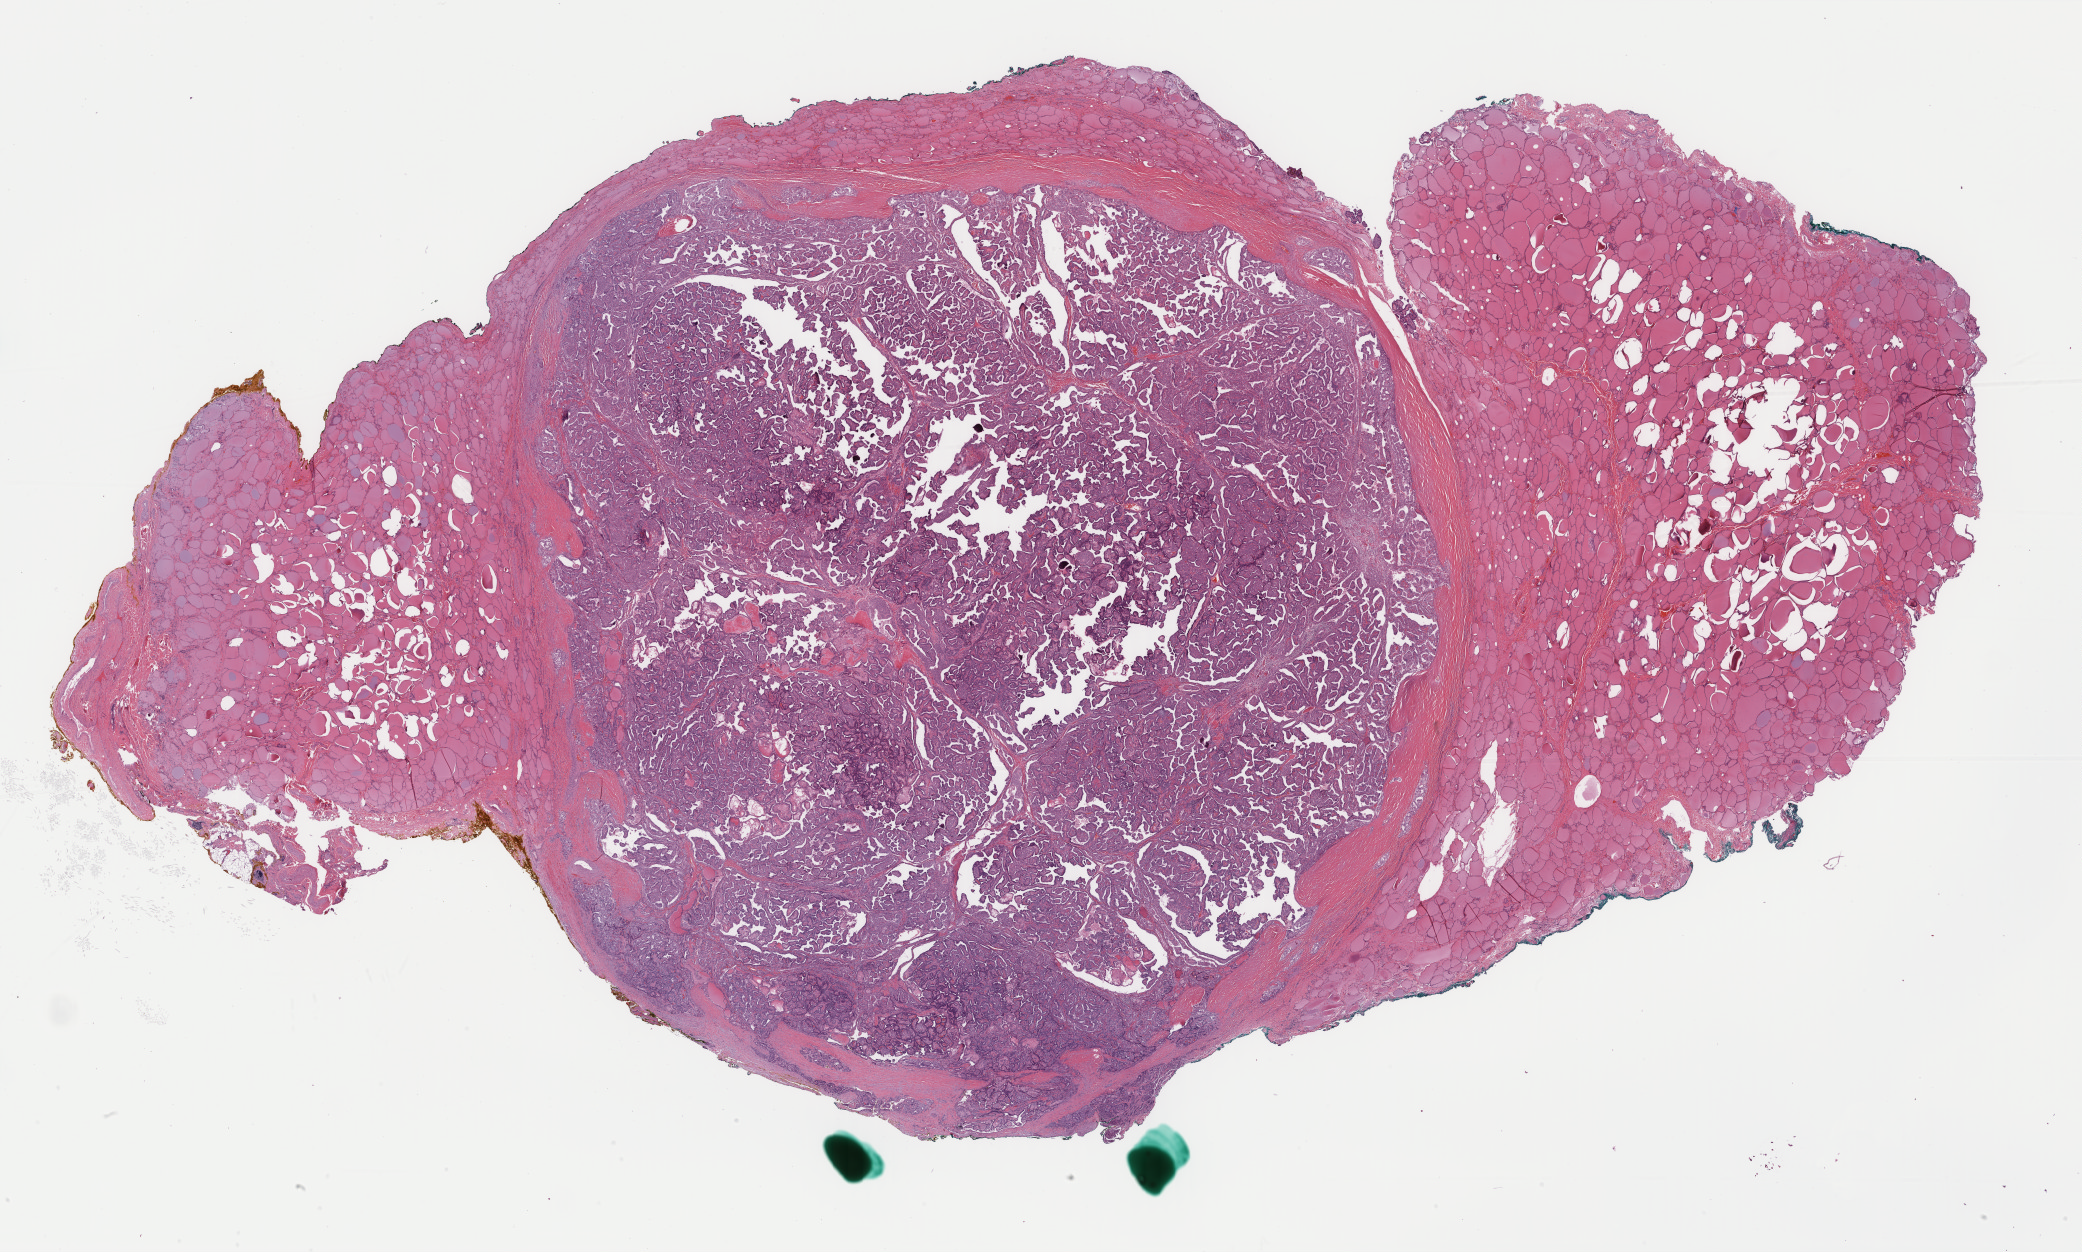
Digitized H&E tissue section (whole slide), low-resolution overview of the scanned area, about 33.1 x 19.9 mm (slide scanned at 40x). Formalin-fixed paraffin-embedded (FFPE) diagnostic section. Primary tumour sample from the thyroid. Female patient; age at initial diagnosis 37 years.
Diagnosis: Papillary adenocarcinoma, NOS (thyroid gland). AJCC pathologic stage: I (7th edition). TNM: T2 N0 M0.